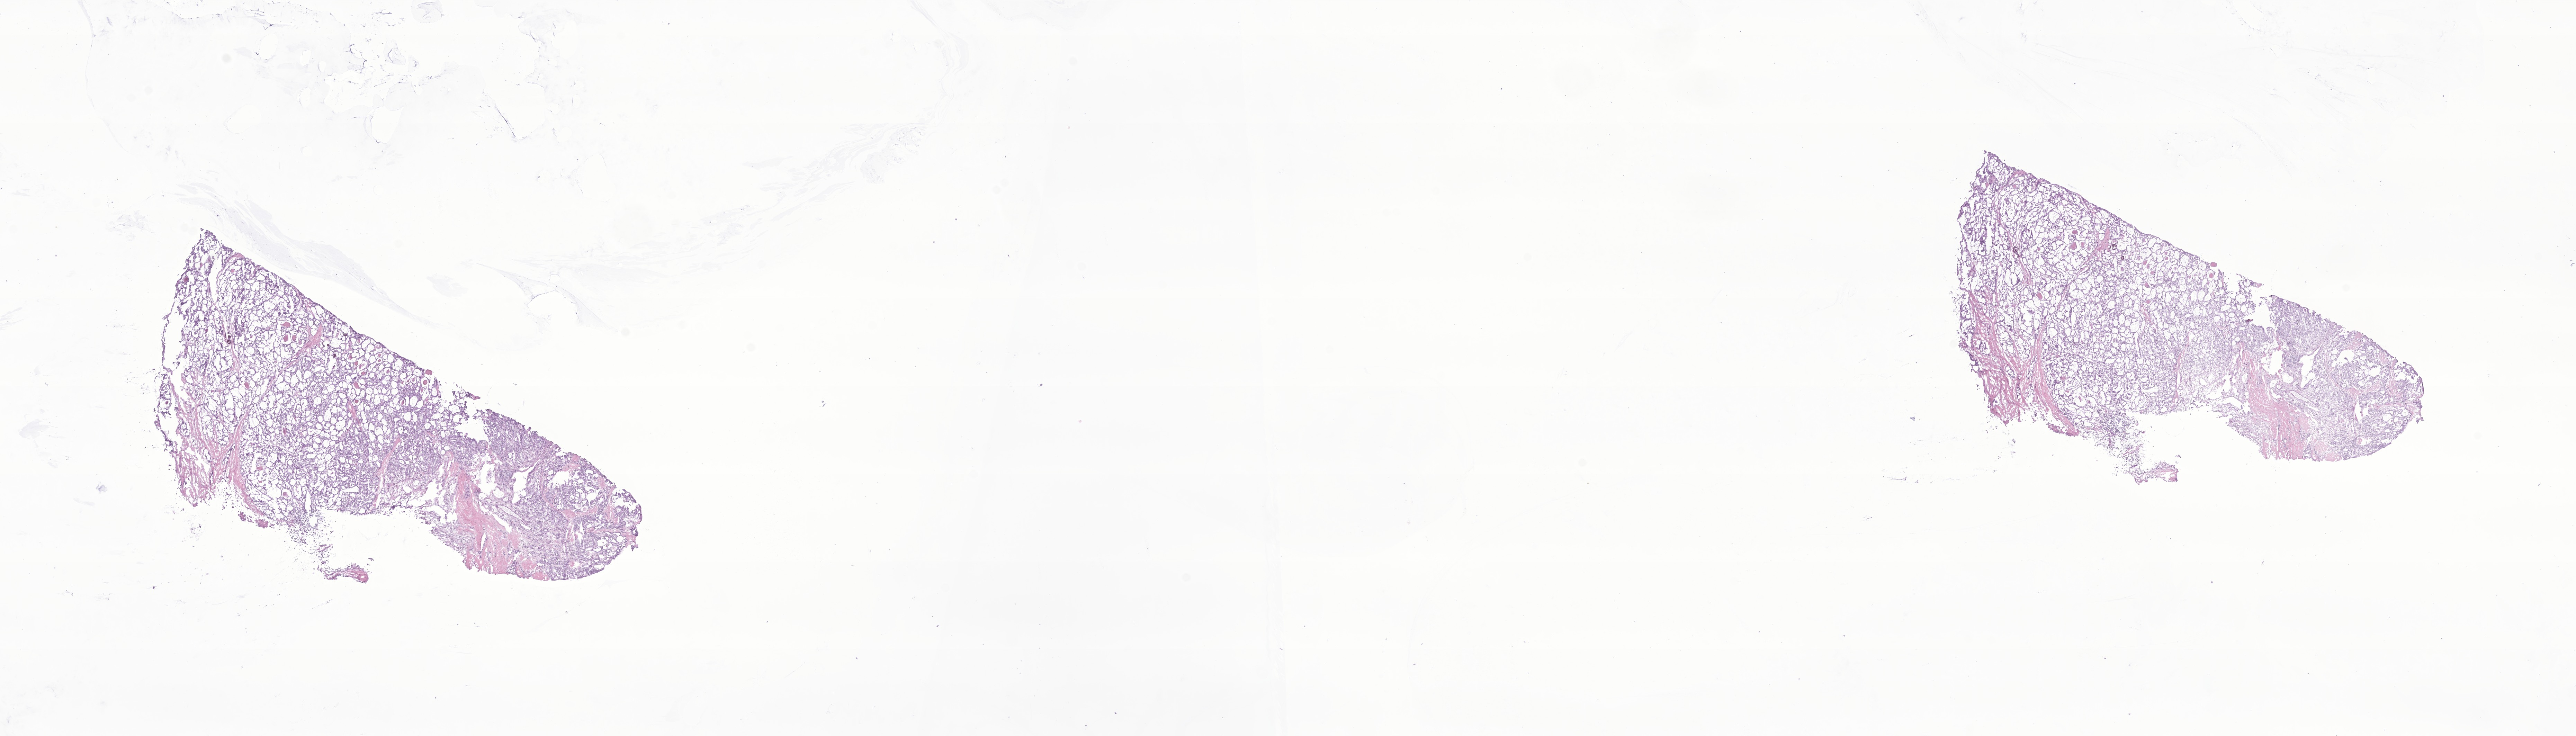
Digitized H&E-stained section of tumor tissue from the thyroid, a low-resolution overview of the entire scanned area, about 31.4 x 9.0 mm; cryosection (OCT / tissue freezing medium). Patient male; age 127 months (10 years 7 months).
Diagnosis (ICD-O-3 morphology term): Papillary carcinoma, NOS.